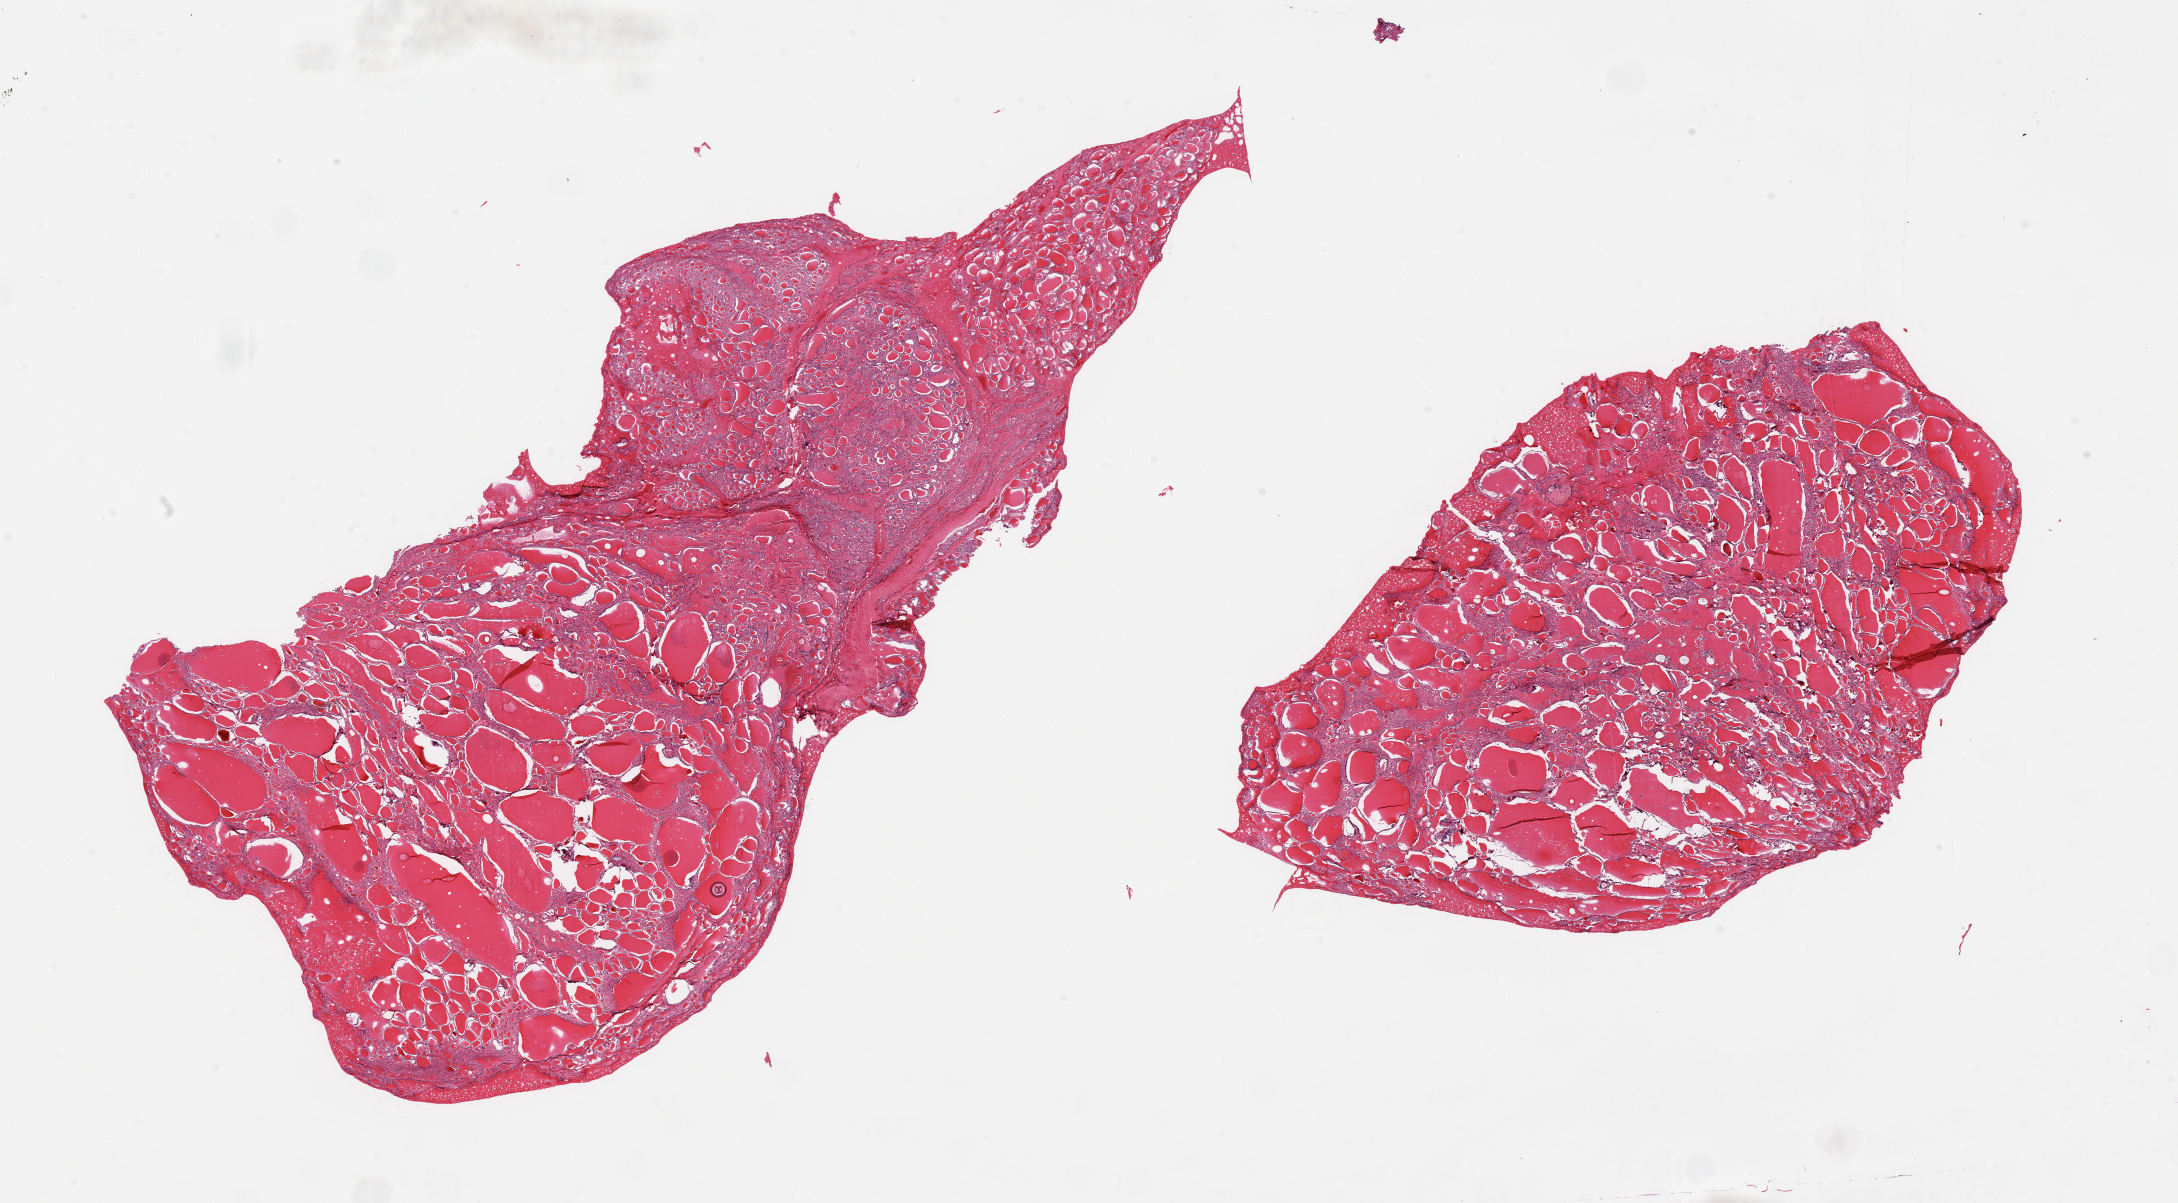
Whole-slide image, hematoxylin and eosin (H&E) stain, shown as a low-resolution overview of the whole scanned area (about 34.5 x 19.0 mm, slide scanned at 20x); PAXgene-fixed paraffin-embedded (PFPE) section; section of thyroid (target tissue); donor tissue sample. Donor sex: male.
- pathologist's review note for this sample: 2 pieces, multinodular hyperplasia